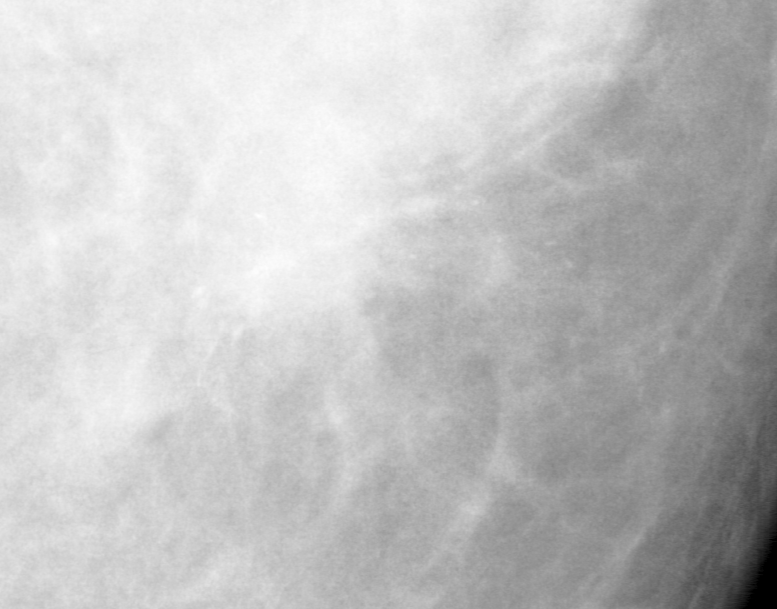
Crop from a digitized film mammogram around one marked abnormality, right breast, CC view.
Marked abnormality: calcifications, morphology pleomorphic, distribution clustered; BI-RADS assessment category 5; pathology result (as recorded, not read from the image): malignant.